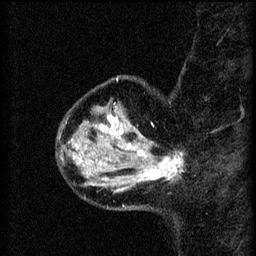
Breast MRI (dynamic contrast-enhanced), one sagittal slice; slice 14 of 60 in the series (ordered by position); 3 images stored at this slice position (order not interpretable as contrast timing); 1.5 T; TE 4.2 ms, TR 8.2 ms; 256 × 256 image matrix, field of view 180 × 180 mm. Patient: female, 37 years.
Outlined on this slice (semi-automatically segmented with operator editing):
- analysis volume of interest (the breast-tissue region the enhancement analysis was run in; not a lesion): bounding box (x1, y1, x2, y2) in pixels: (124, 138, 185, 191)
- tumour enhancement mask (voxels above the 70 % enhancement threshold inside the analysis volume of interest): (124, 150, 183, 189)